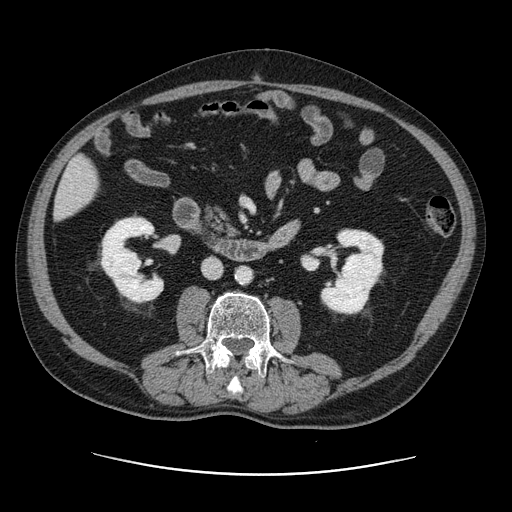
Contrast-enhanced abdominal CT, one axial slice; slice 33 of 141 in the series (ordered by position); 120 kVp; intravenous contrast given; soft-tissue window (W 400 / L 40 HU); 2.5 mm slice thickness; 512 × 512 image matrix, field of view 395 × 395 mm. Male patient, age 72 years. From the clinical record (not read from this slice): diagnosis: colorectal cancer liver metastases, imaged before liver resection; multiple liver metastases: yes; largest metastasis: 5.4 cm; disease in both lobes: yes.
Structures marked on this image (manually delineated by an expert):
- liver: bounding box [x1, y1, x2, y2] px = [56, 157, 99, 219]
- planned liver remnant (the part of the liver to remain after resection): [56, 157, 99, 219]